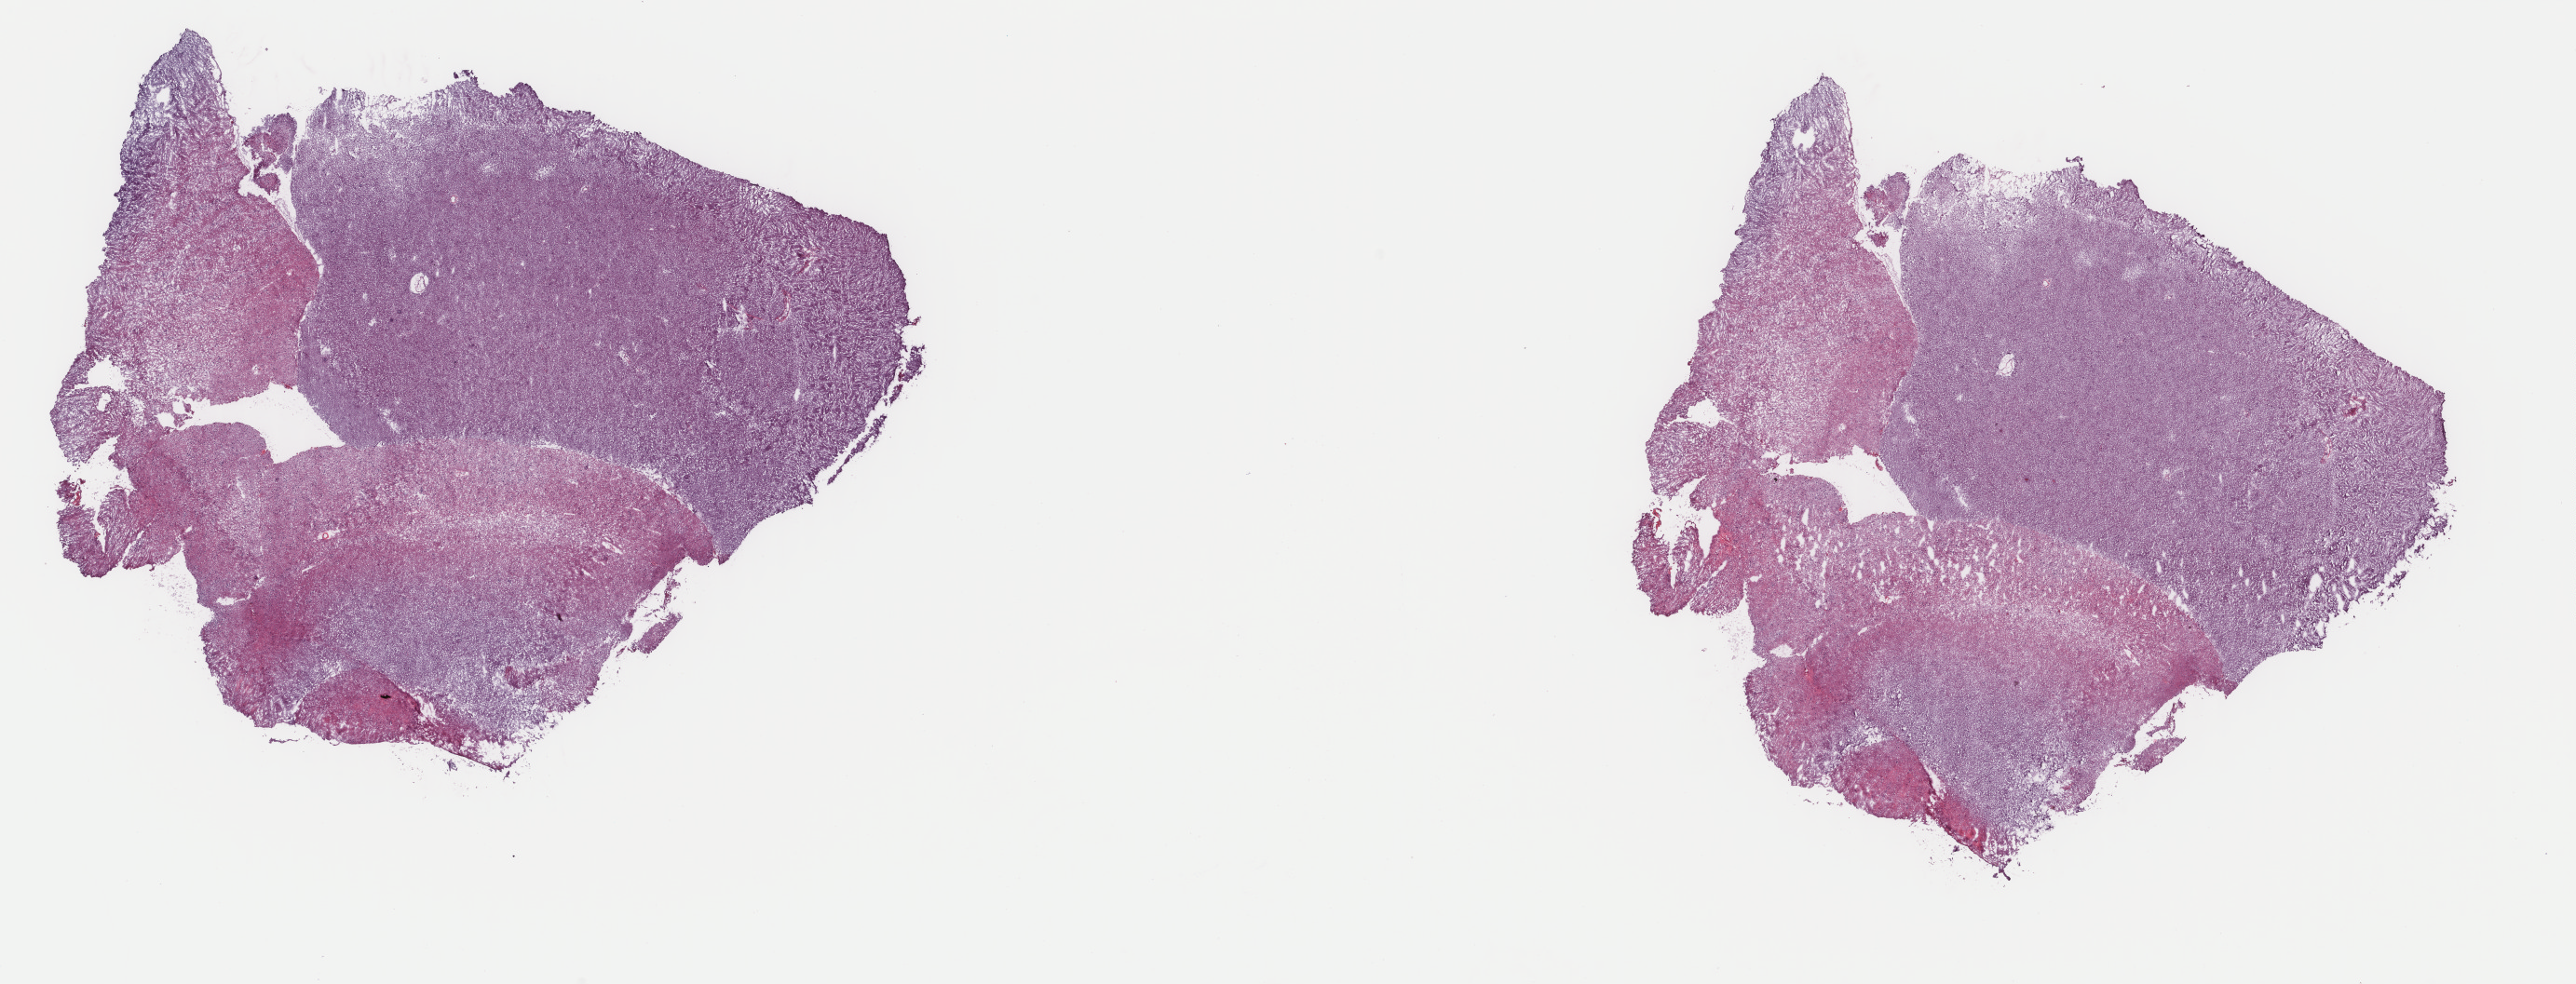
Digitized H&E-stained tissue section (whole slide), low-resolution overview of the scanned area, about 22.0 x 8.4 mm (acquisition: 40x scan). Frozen section from the top of the tissue portion. Brain, primary tumour sample. Female, age 20 years at initial diagnosis. Histologic grade: G2 (moderately differentiated). Pathologist review of this section (percent, as recorded): tumour cells 20%, tumour nuclei 70%, normal cells 70%, stromal cells 10%, necrosis 0%. Infiltration values recorded for this section: lymphocyte infiltration 0%, monocyte infiltration 0%, neutrophil infiltration 0%.
• laterality: left
• pathologic diagnosis: Oligodendroglioma, NOS (cerebrum)